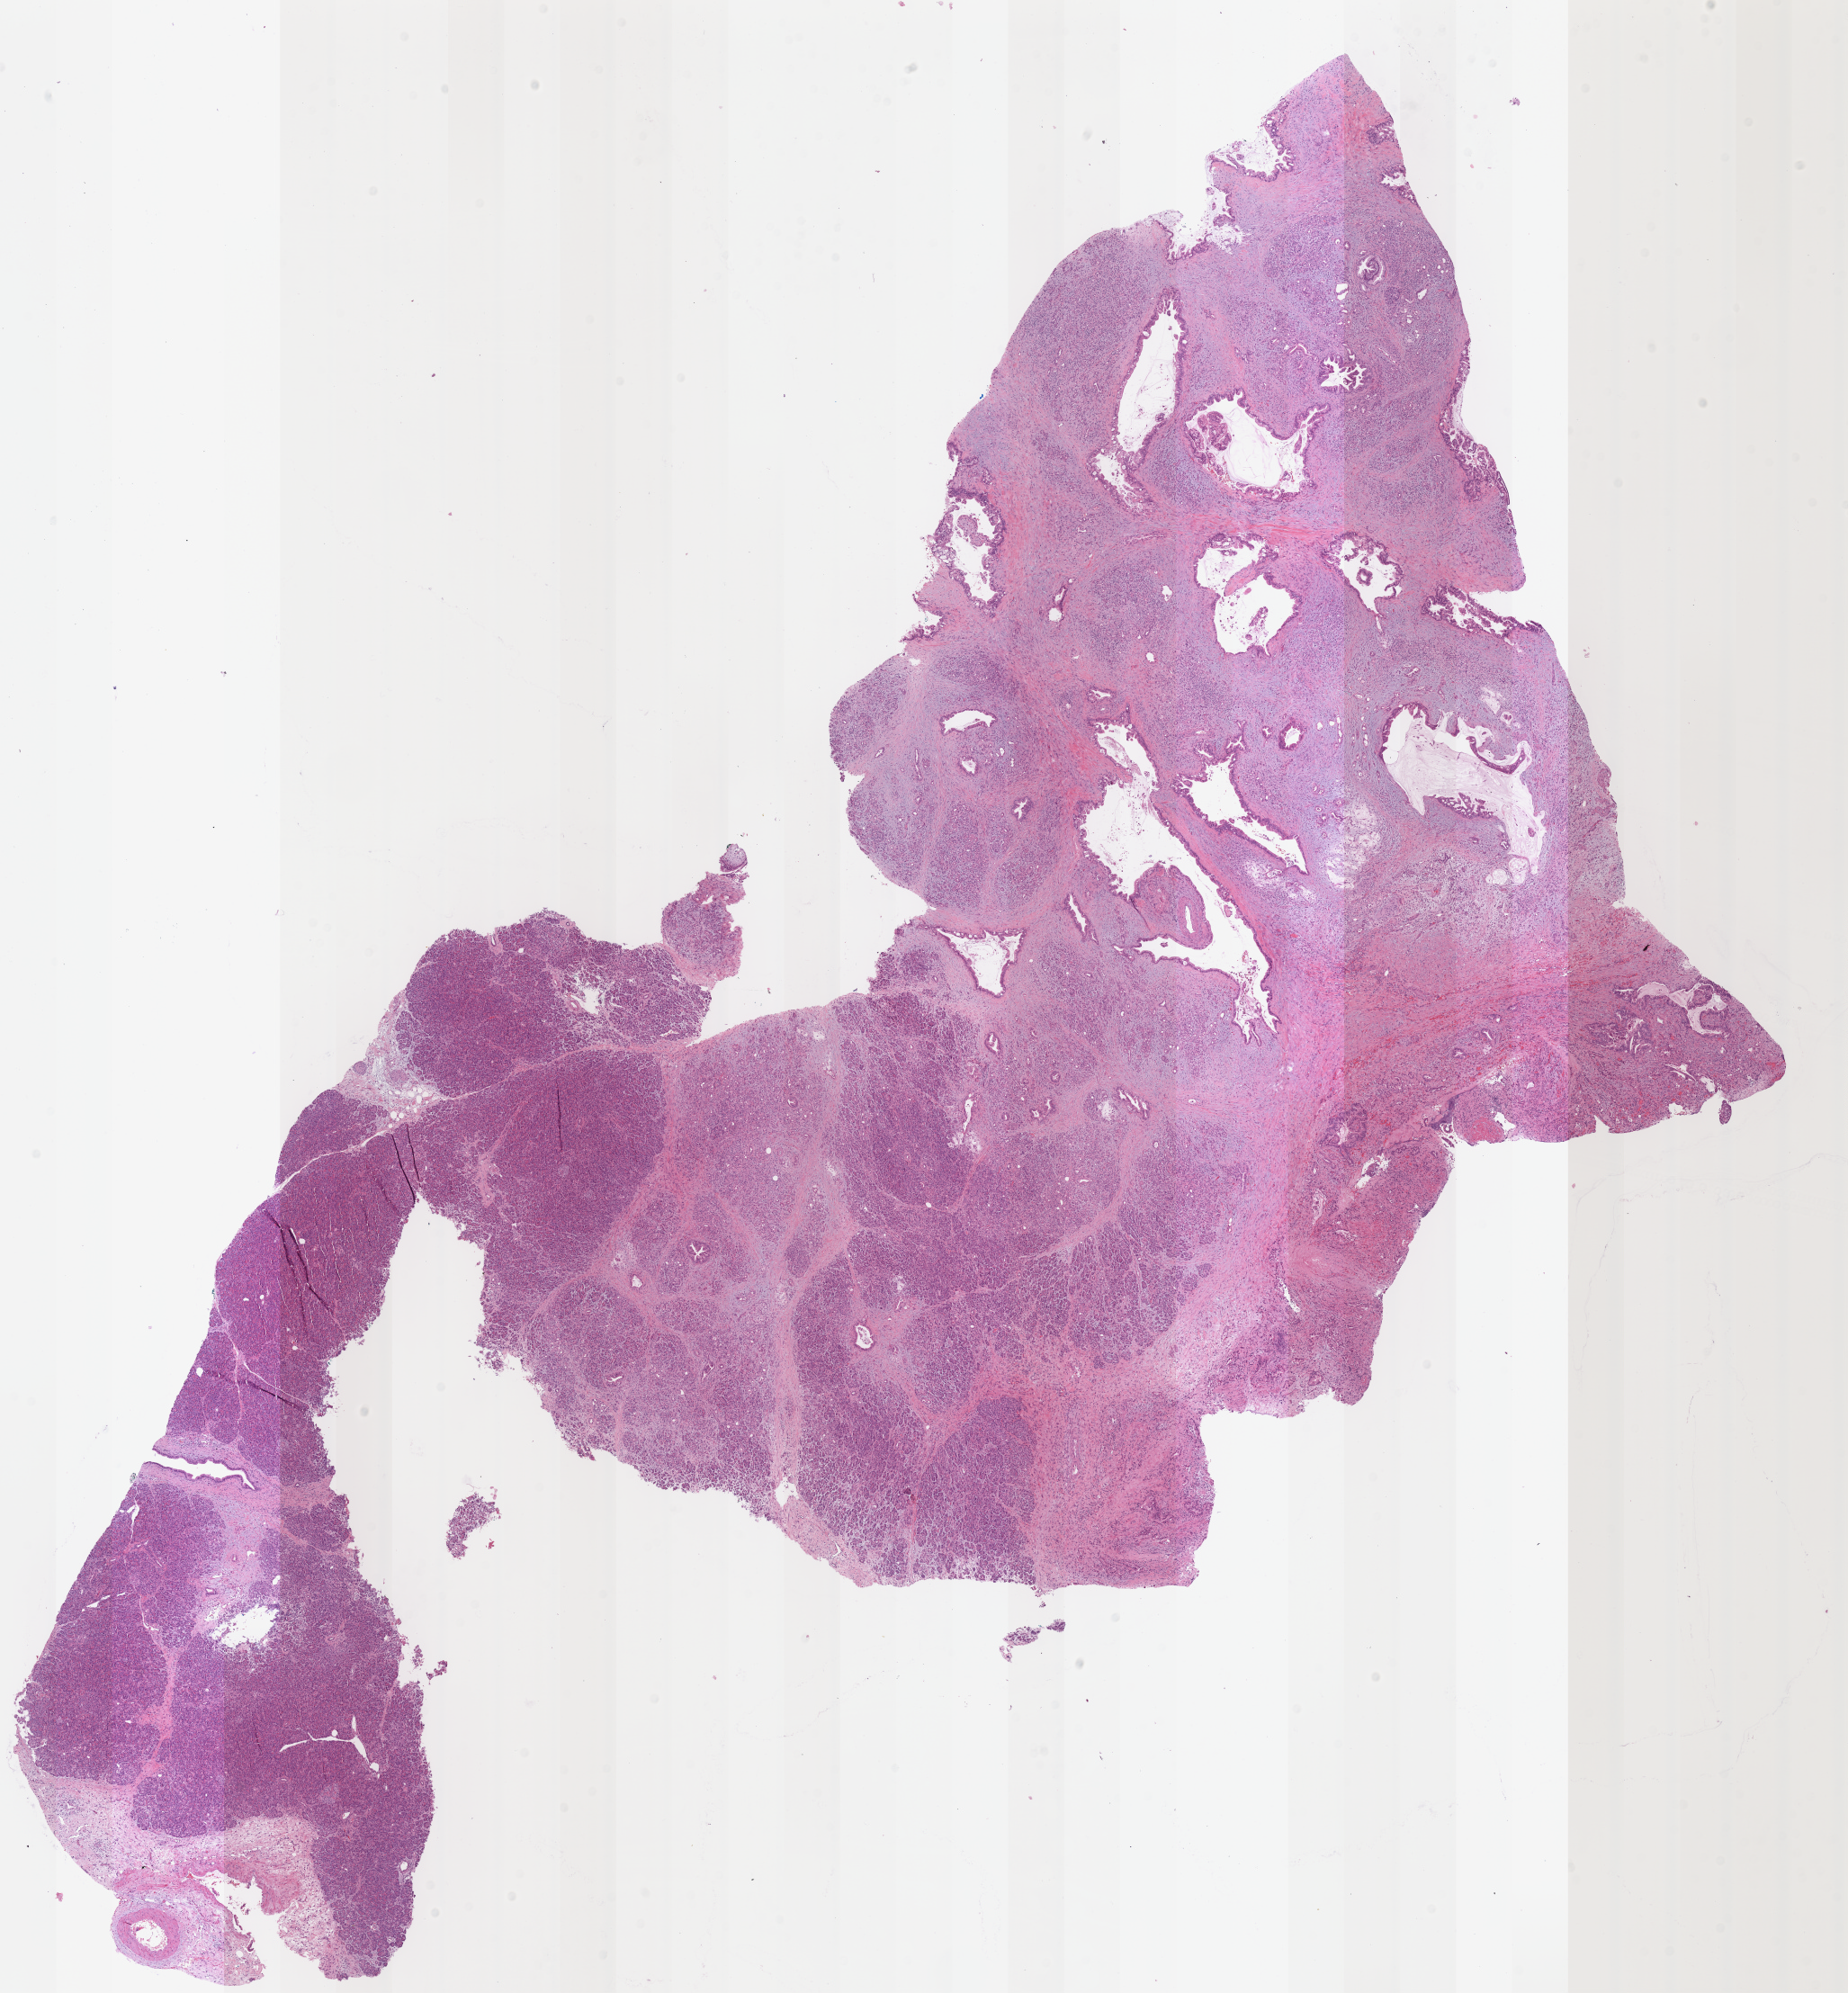
Digitized Hematoxylin and eosin (H&E) stained tissue section (whole slide), shown as a low-resolution overview of the whole scanned area (about 16.2 x 17.4 mm, slide scanned at 40x). Formalin-fixed paraffin-embedded (FFPE) diagnostic section. Primary tumour sample from the pancreas. Patient: female, age at initial diagnosis 69 years.
Histologic diagnosis: Infiltrating duct carcinoma, NOS (head of pancreas).